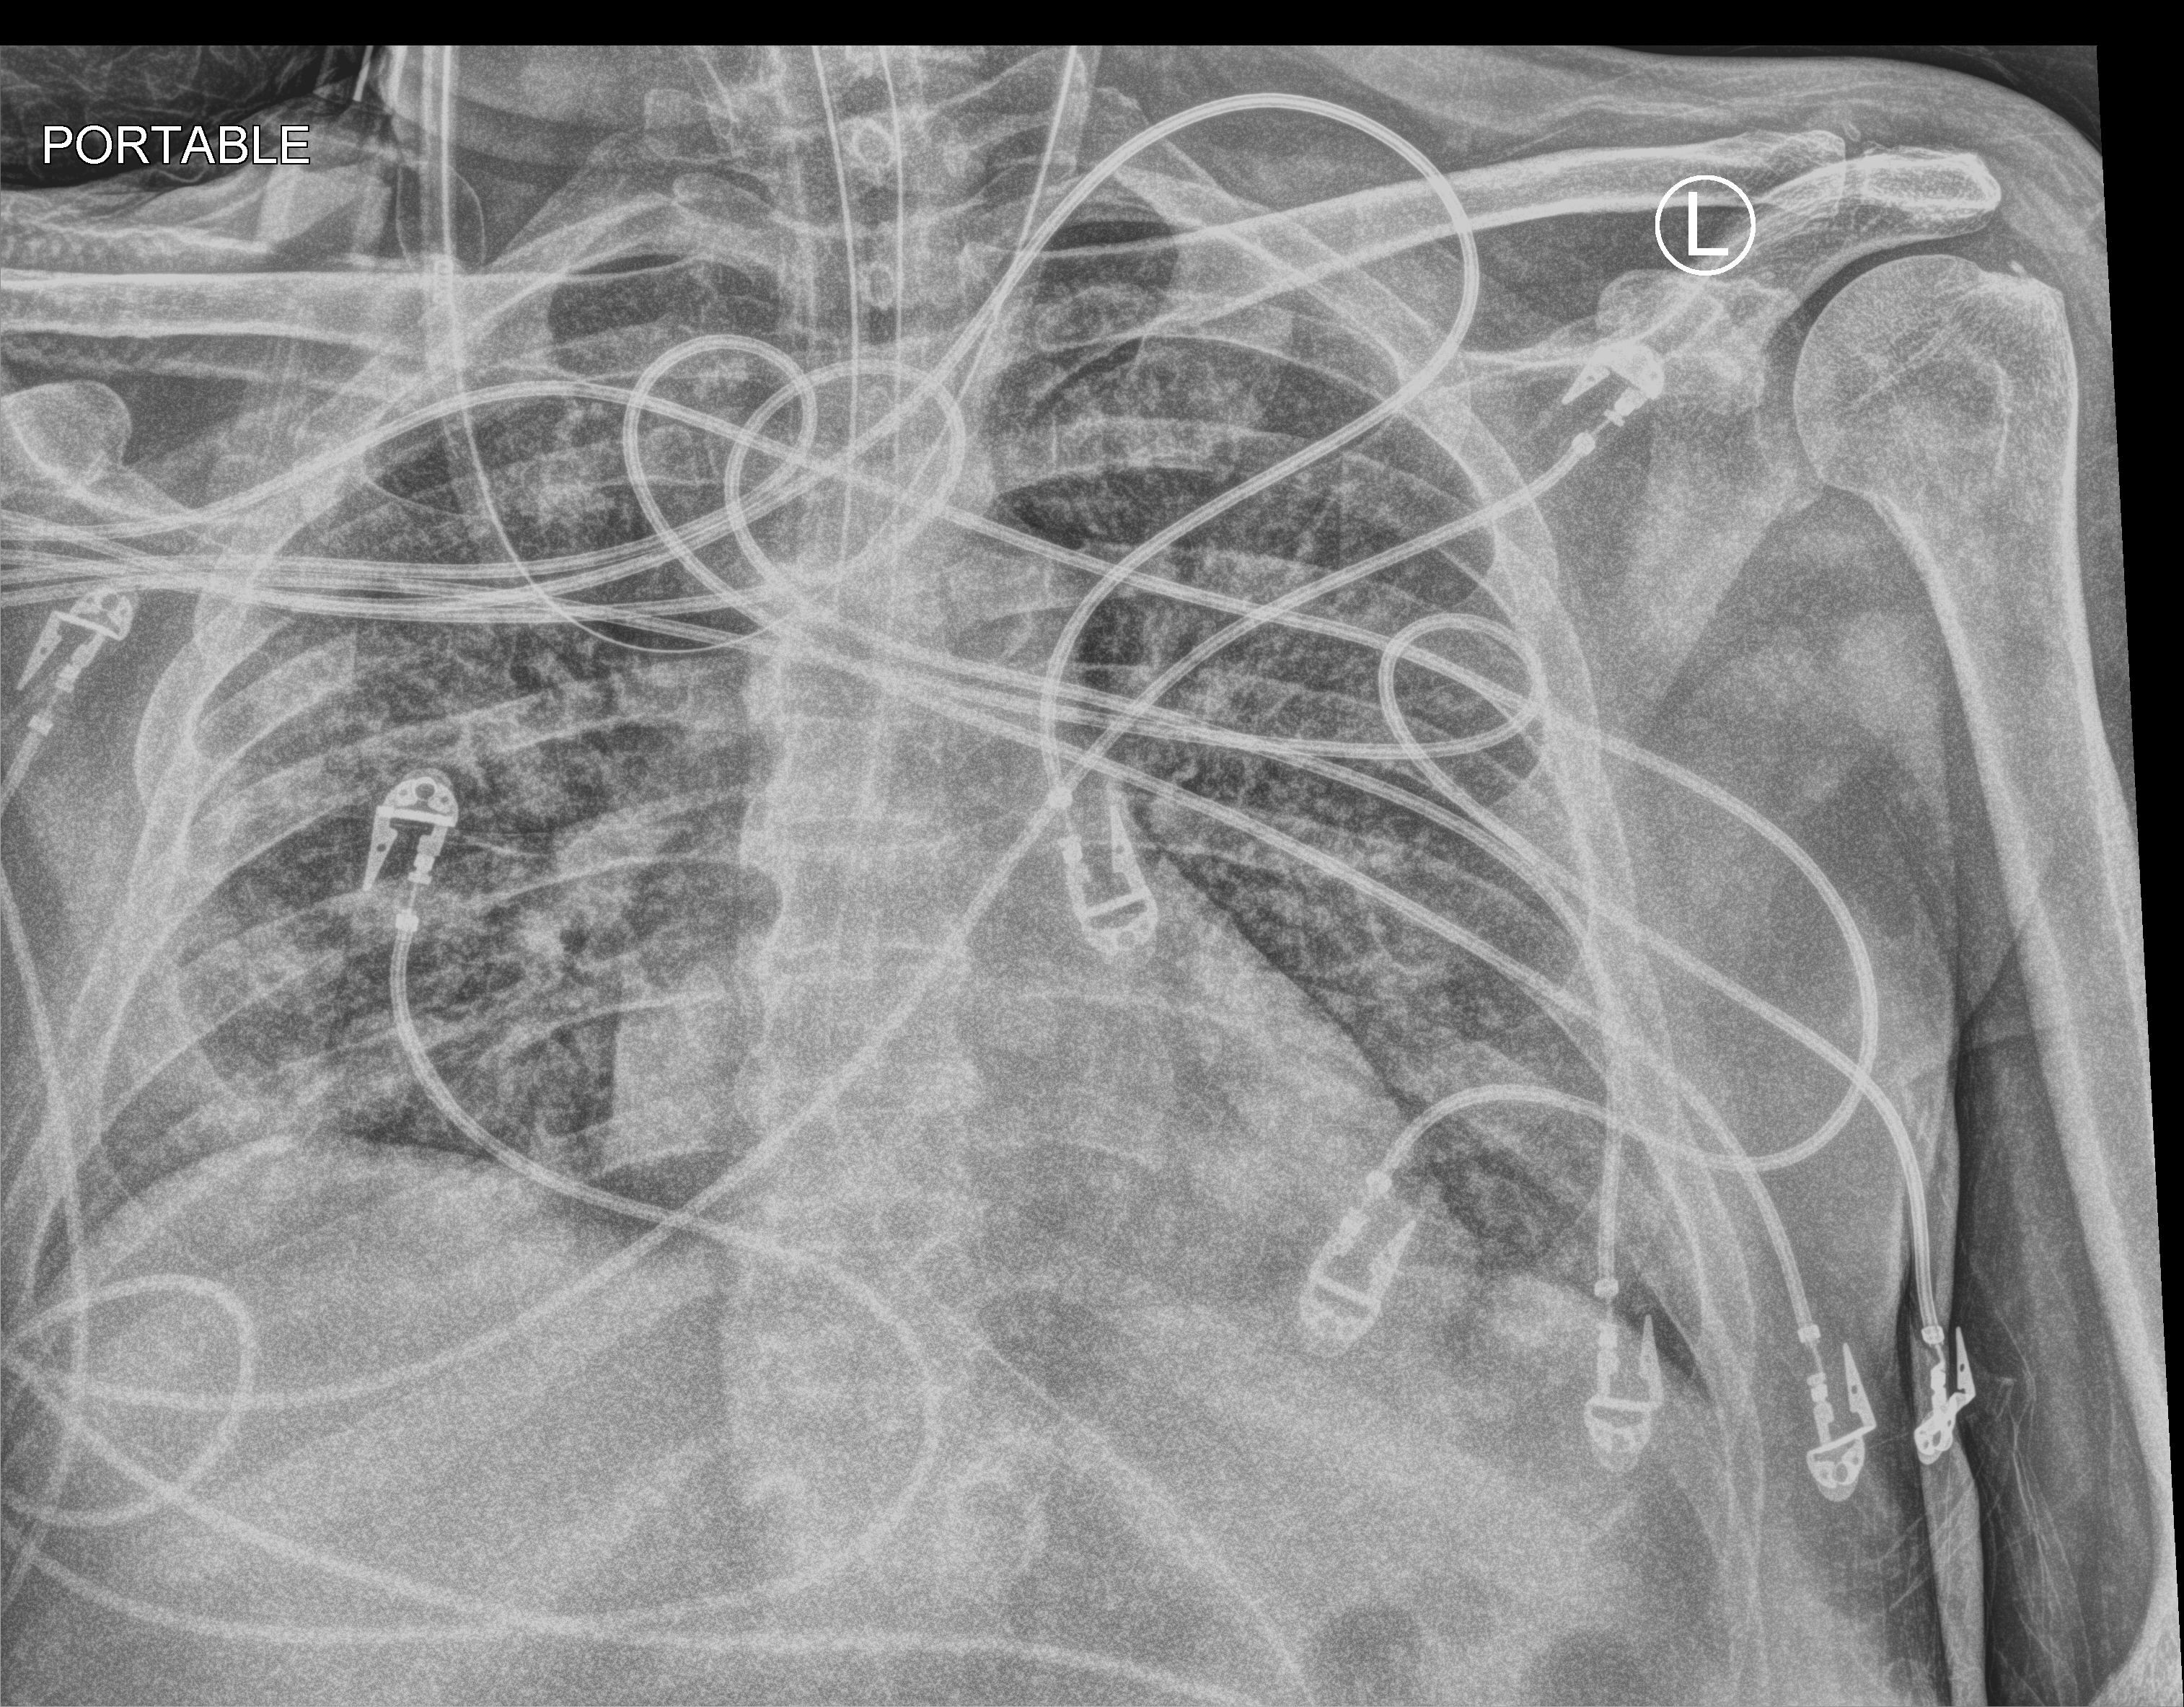
Bedside chest radiograph (computed radiography), anteroposterior (AP) projection. Patient hospitalised with COVID-19; male, aged 60–74 years.
Admission-level facts for this patient (not findings on this image; timing relative to this image not recorded):
- diabetes (admission record): yes